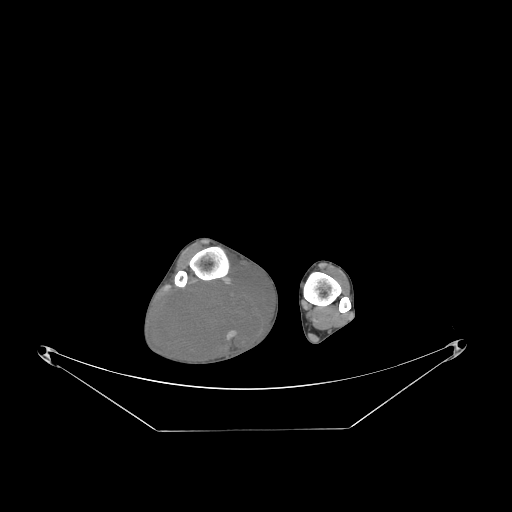
CT of an extremity soft-tissue mass (from a PET/CT study), one axial slice. Slice 56 of 267 in the series (ordered by position). 140 kVp. Soft-tissue window (W 400 / L 40 HU). 3.75 mm slice thickness. 512 × 512 image matrix, field of view 500 × 500 mm. Male patient. Case-level facts recorded for this patient, not image findings: histological type: liposarcoma - round cell; grade: high; site of the primary tumour: right calf.
Outlined on this slice (expert contour drawn on MRI and transferred to this co-registered scan by the dataset authors):
- gross tumour volume (mass): bounding box <155,269,275,366> (left, top, right, bottom; pixels)